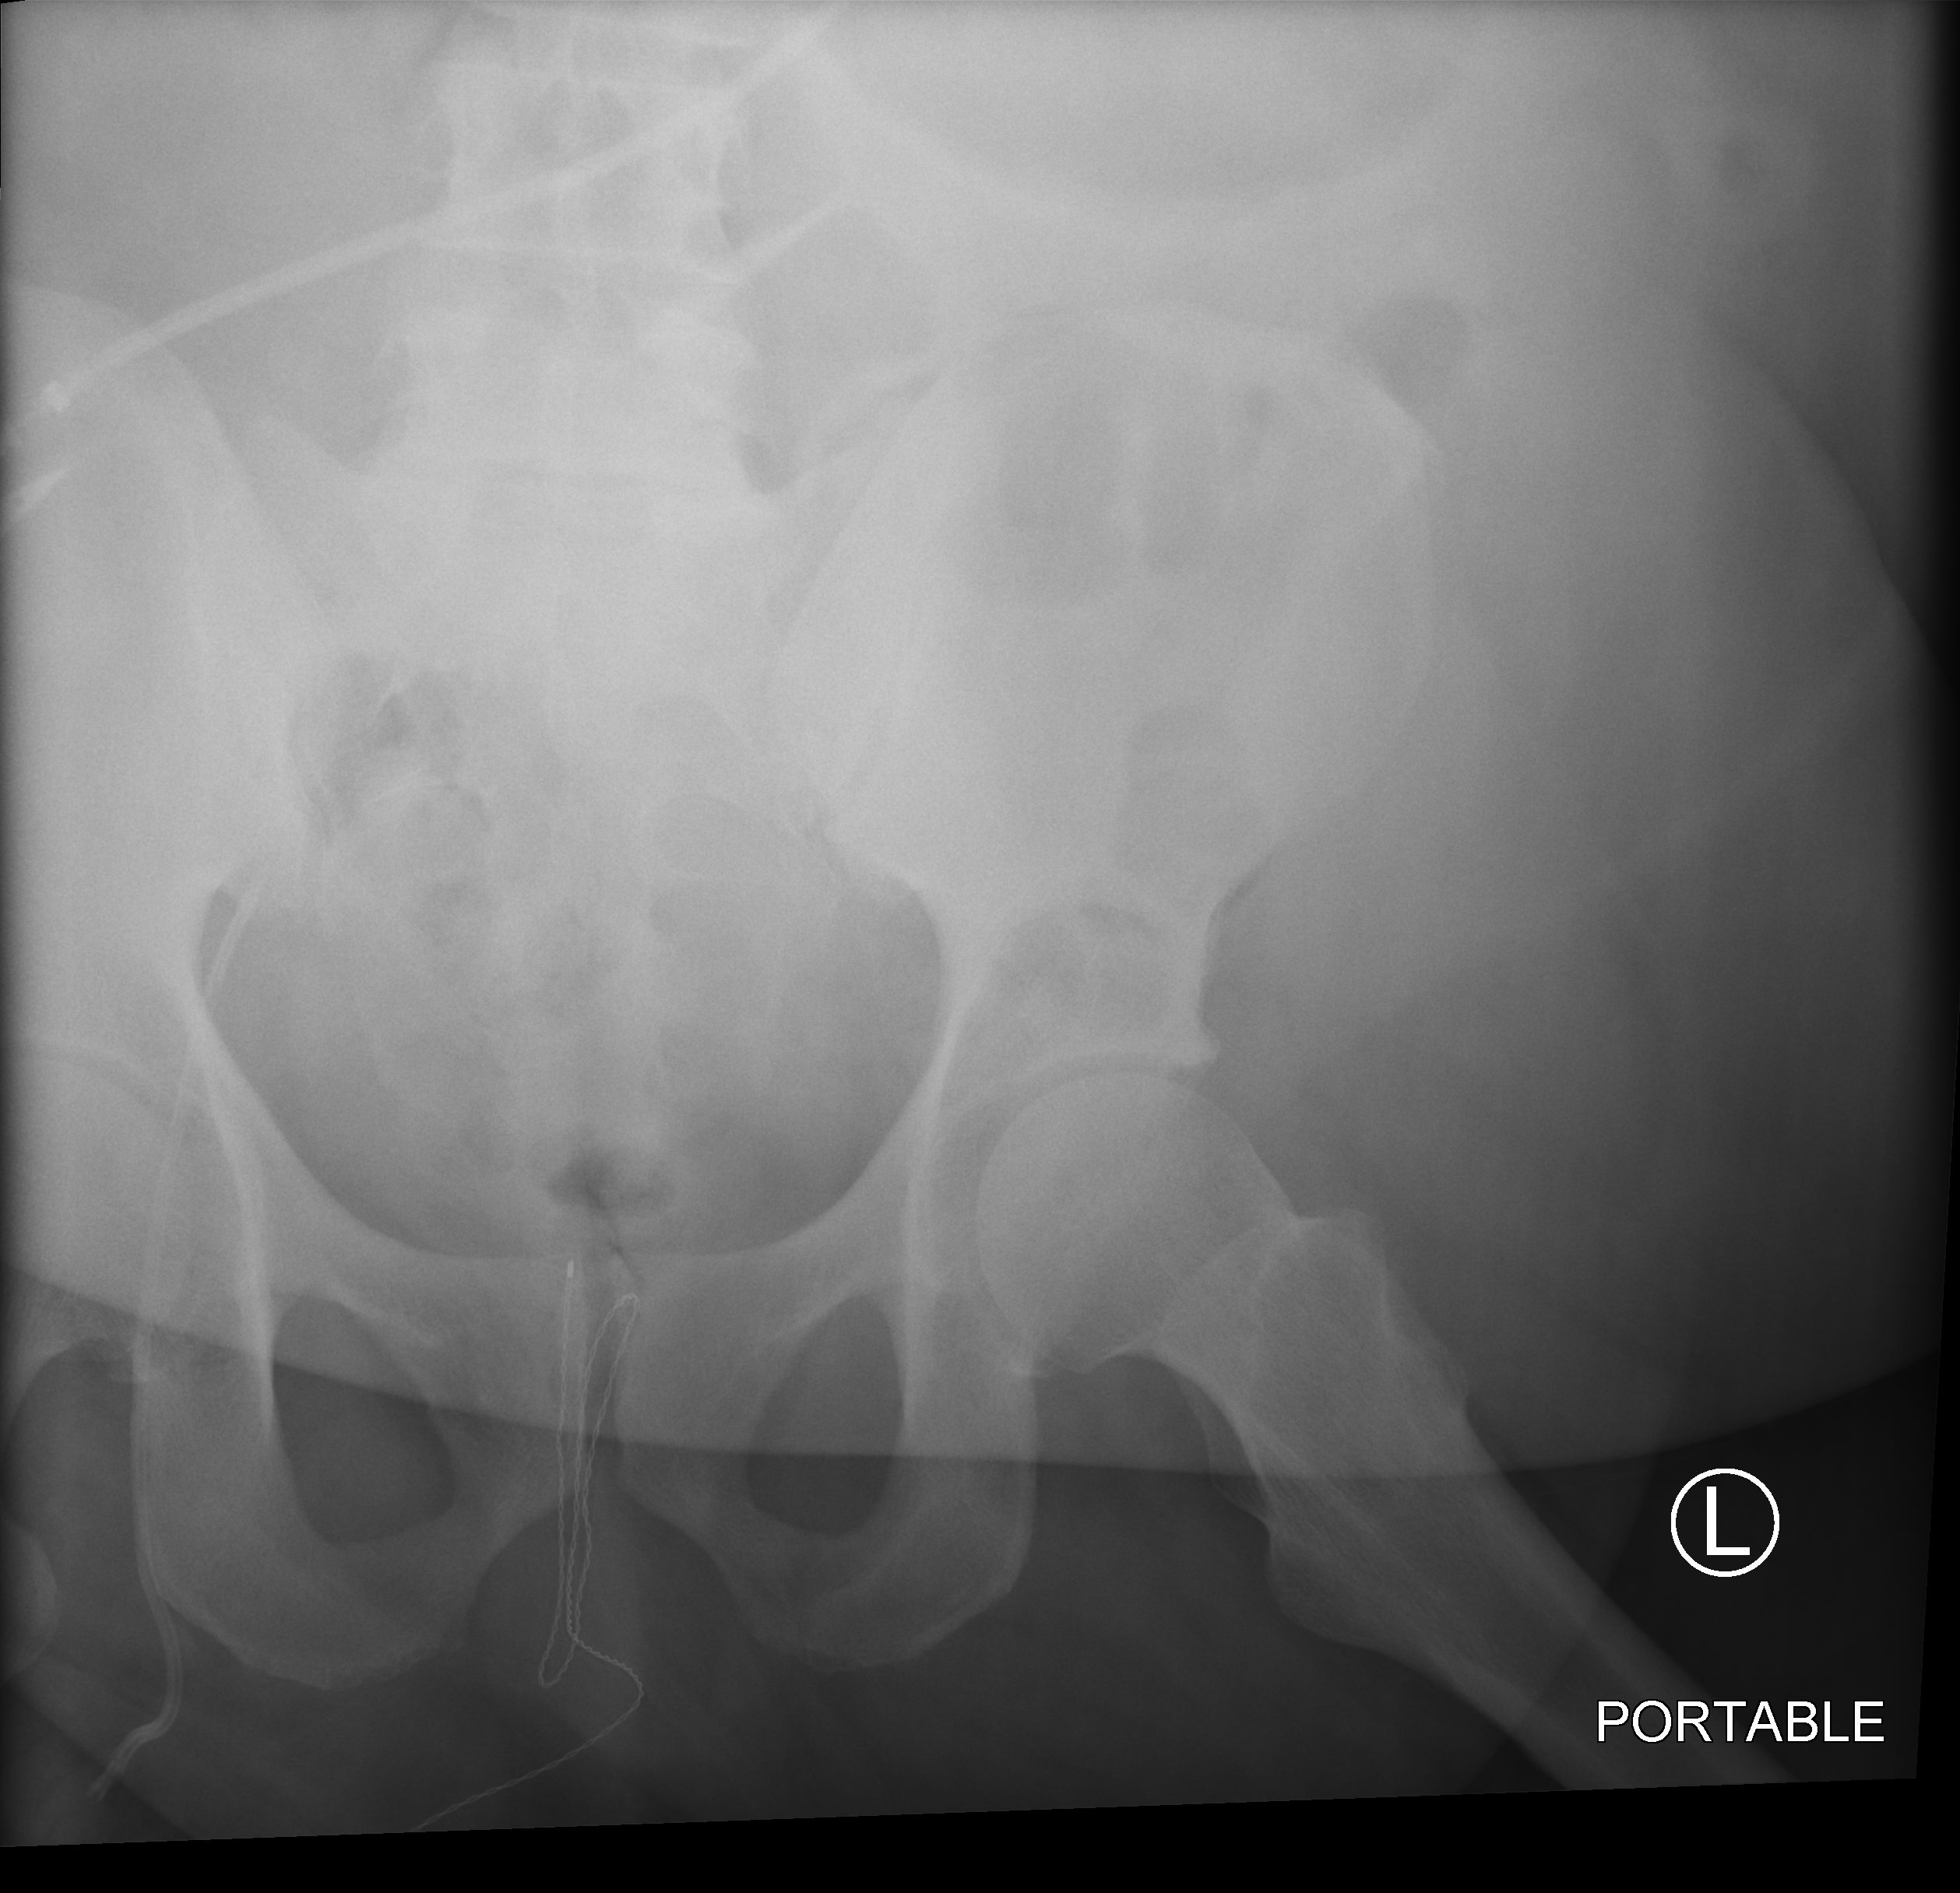
Portable abdomen radiograph, anteroposterior (AP) projection. Patient hospitalised with COVID-19; male, aged 60–74 years.
Hospital-stay facts (about this admission, not read from this image; timing relative to this image not recorded): diabetes (admission record): no.